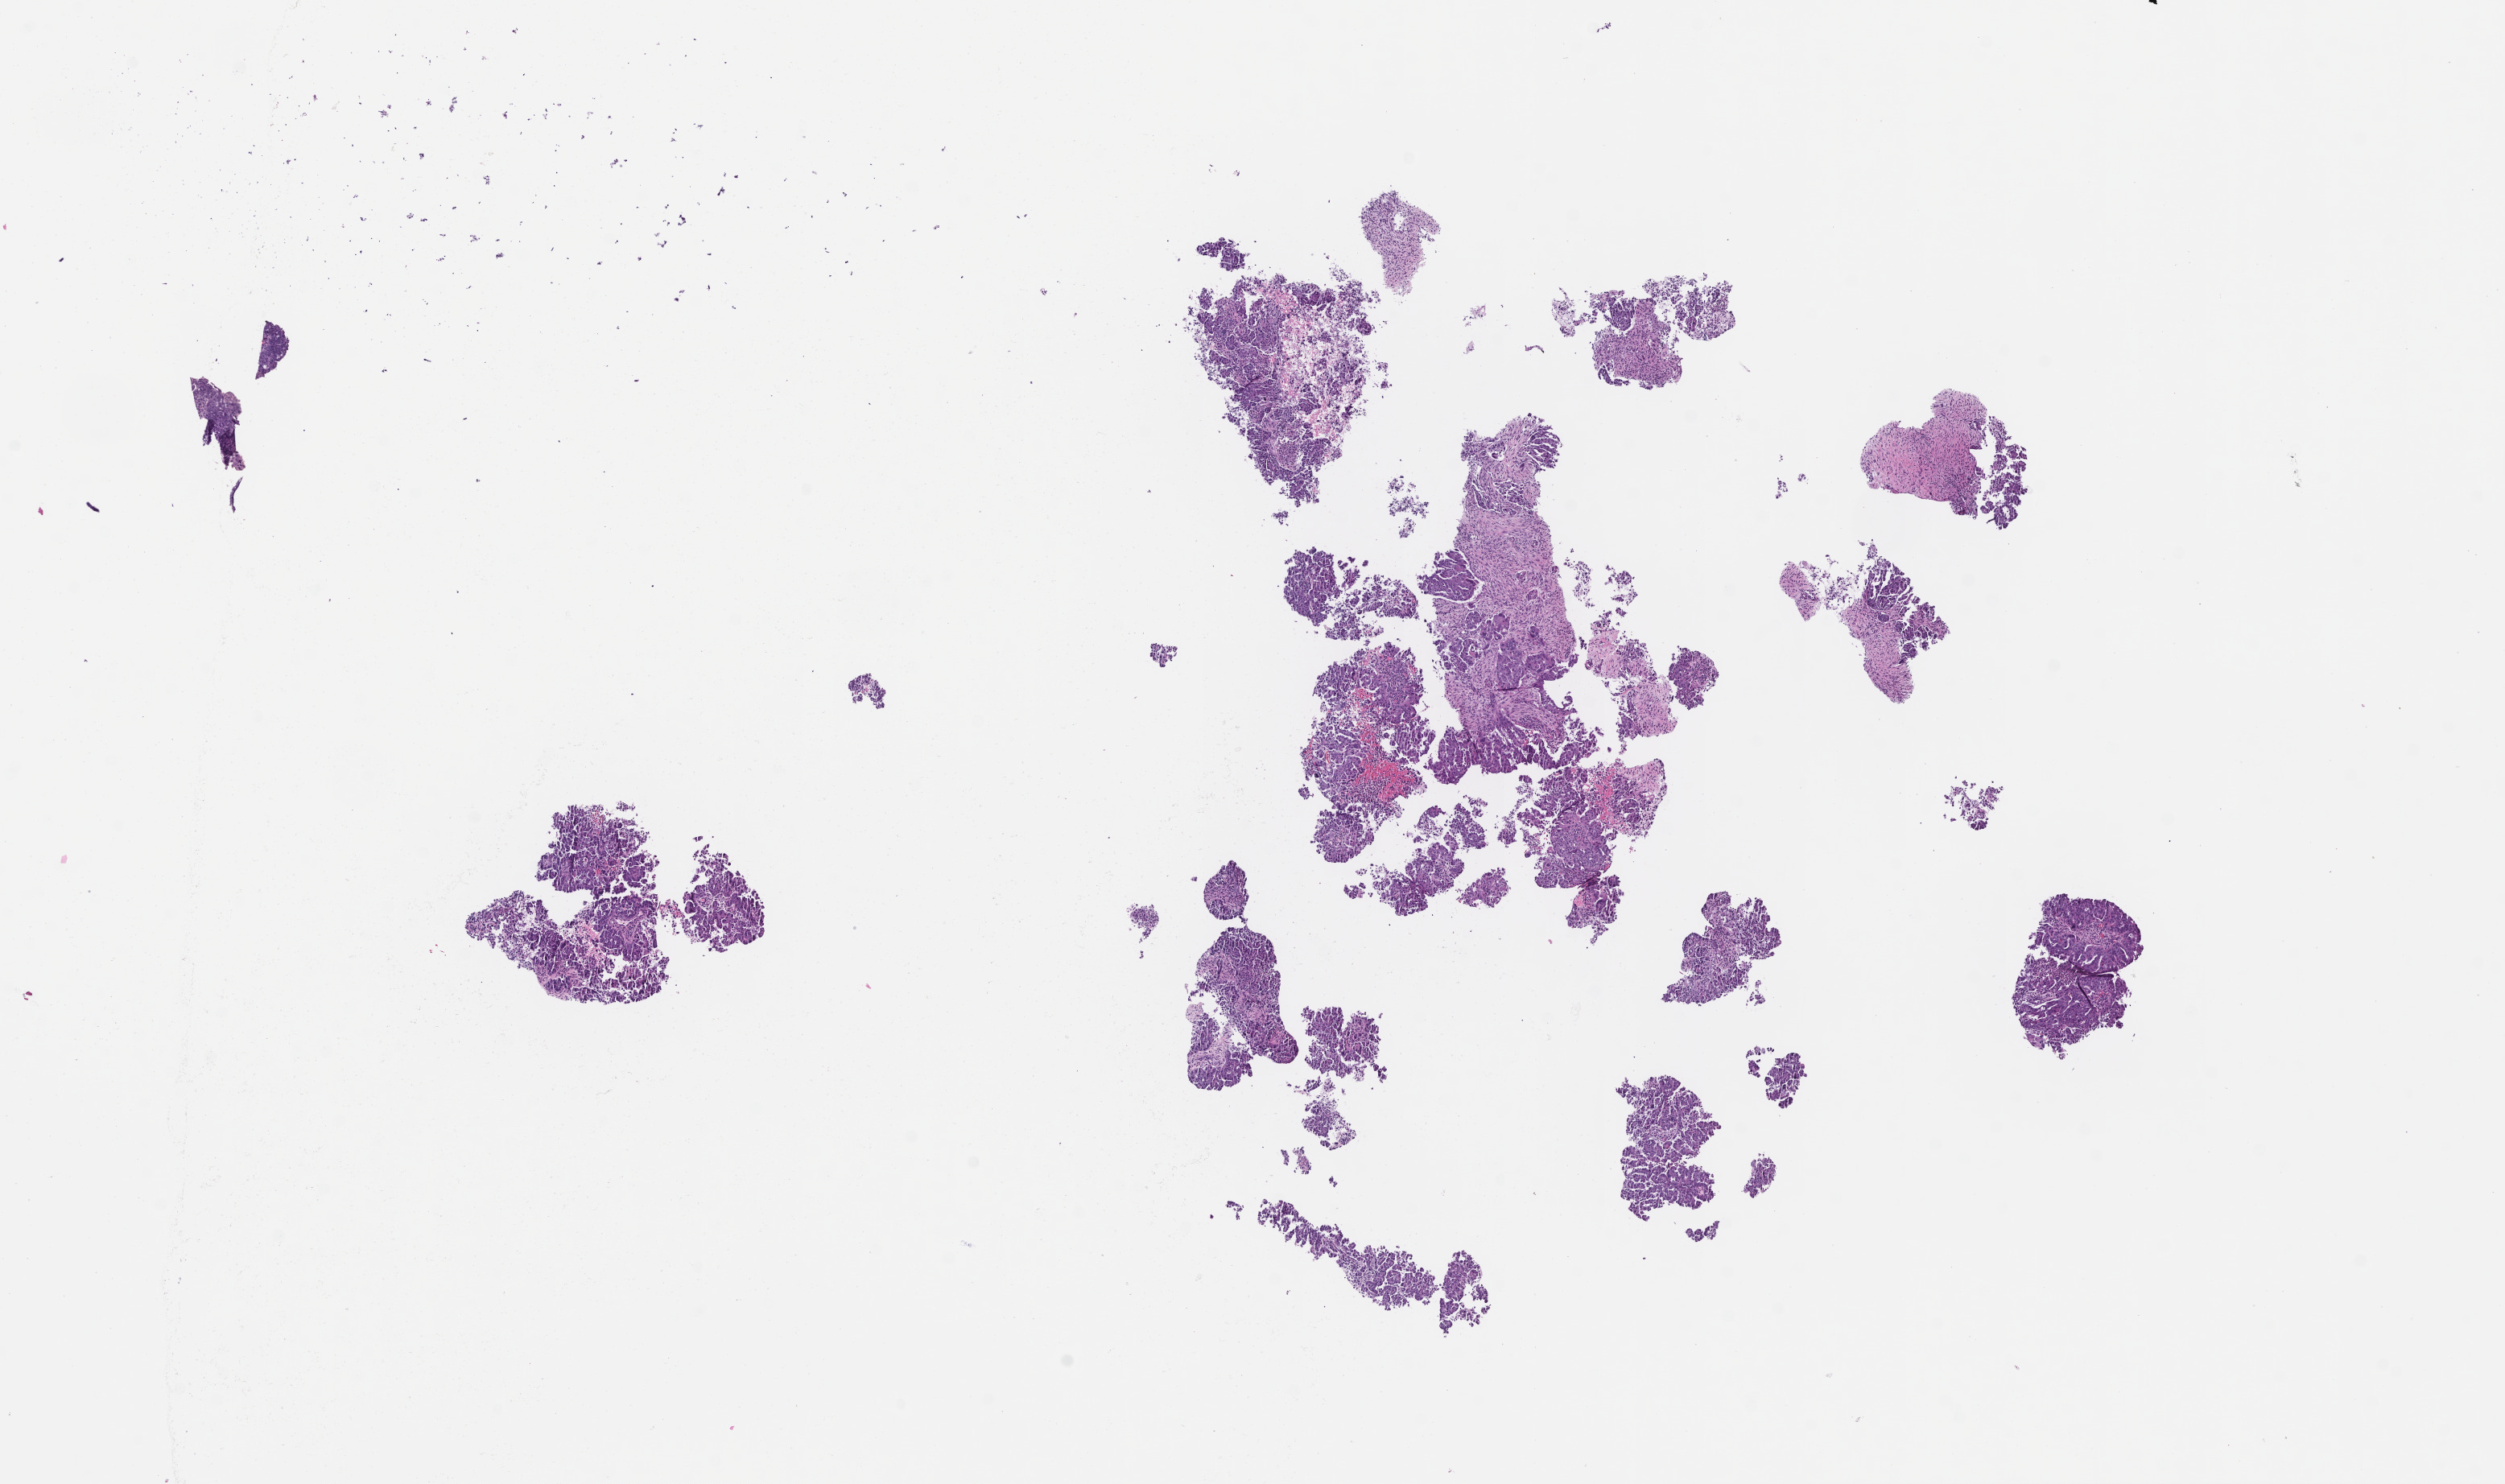
Digitized haematoxylin and eosin-stained section, shown as a low-resolution overview of the whole scanned area (about 12.6 x 7.4 mm), FFPE section. Patient: female.
This section: metastatic tumor tissue. Primary diagnosis of the patient: Ovarian Carcinoma.